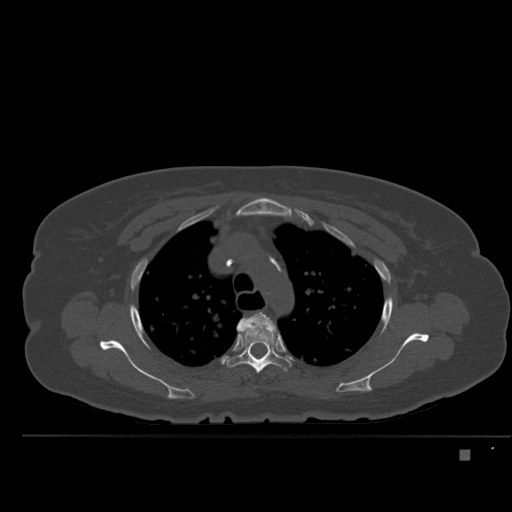
CT including the spine, one axial slice; slice 370 of 477 in the series (ordered by position); bone window (W 1800 / L 400 HU); 1.5 mm slice thickness; 512 × 512 image matrix, field of view 422 × 422 mm. Female patient, age 74 years. Case-level facts recorded for this patient, not image findings: primary cancer: colon.
Outlined on this slice (semi-automatic segmentation, software-assisted and operator-edited):
- T3 vertebra: bounding box <236,312,279,371> (left, top, right, bottom; pixels)
- T4 vertebra: <227,322,291,374>